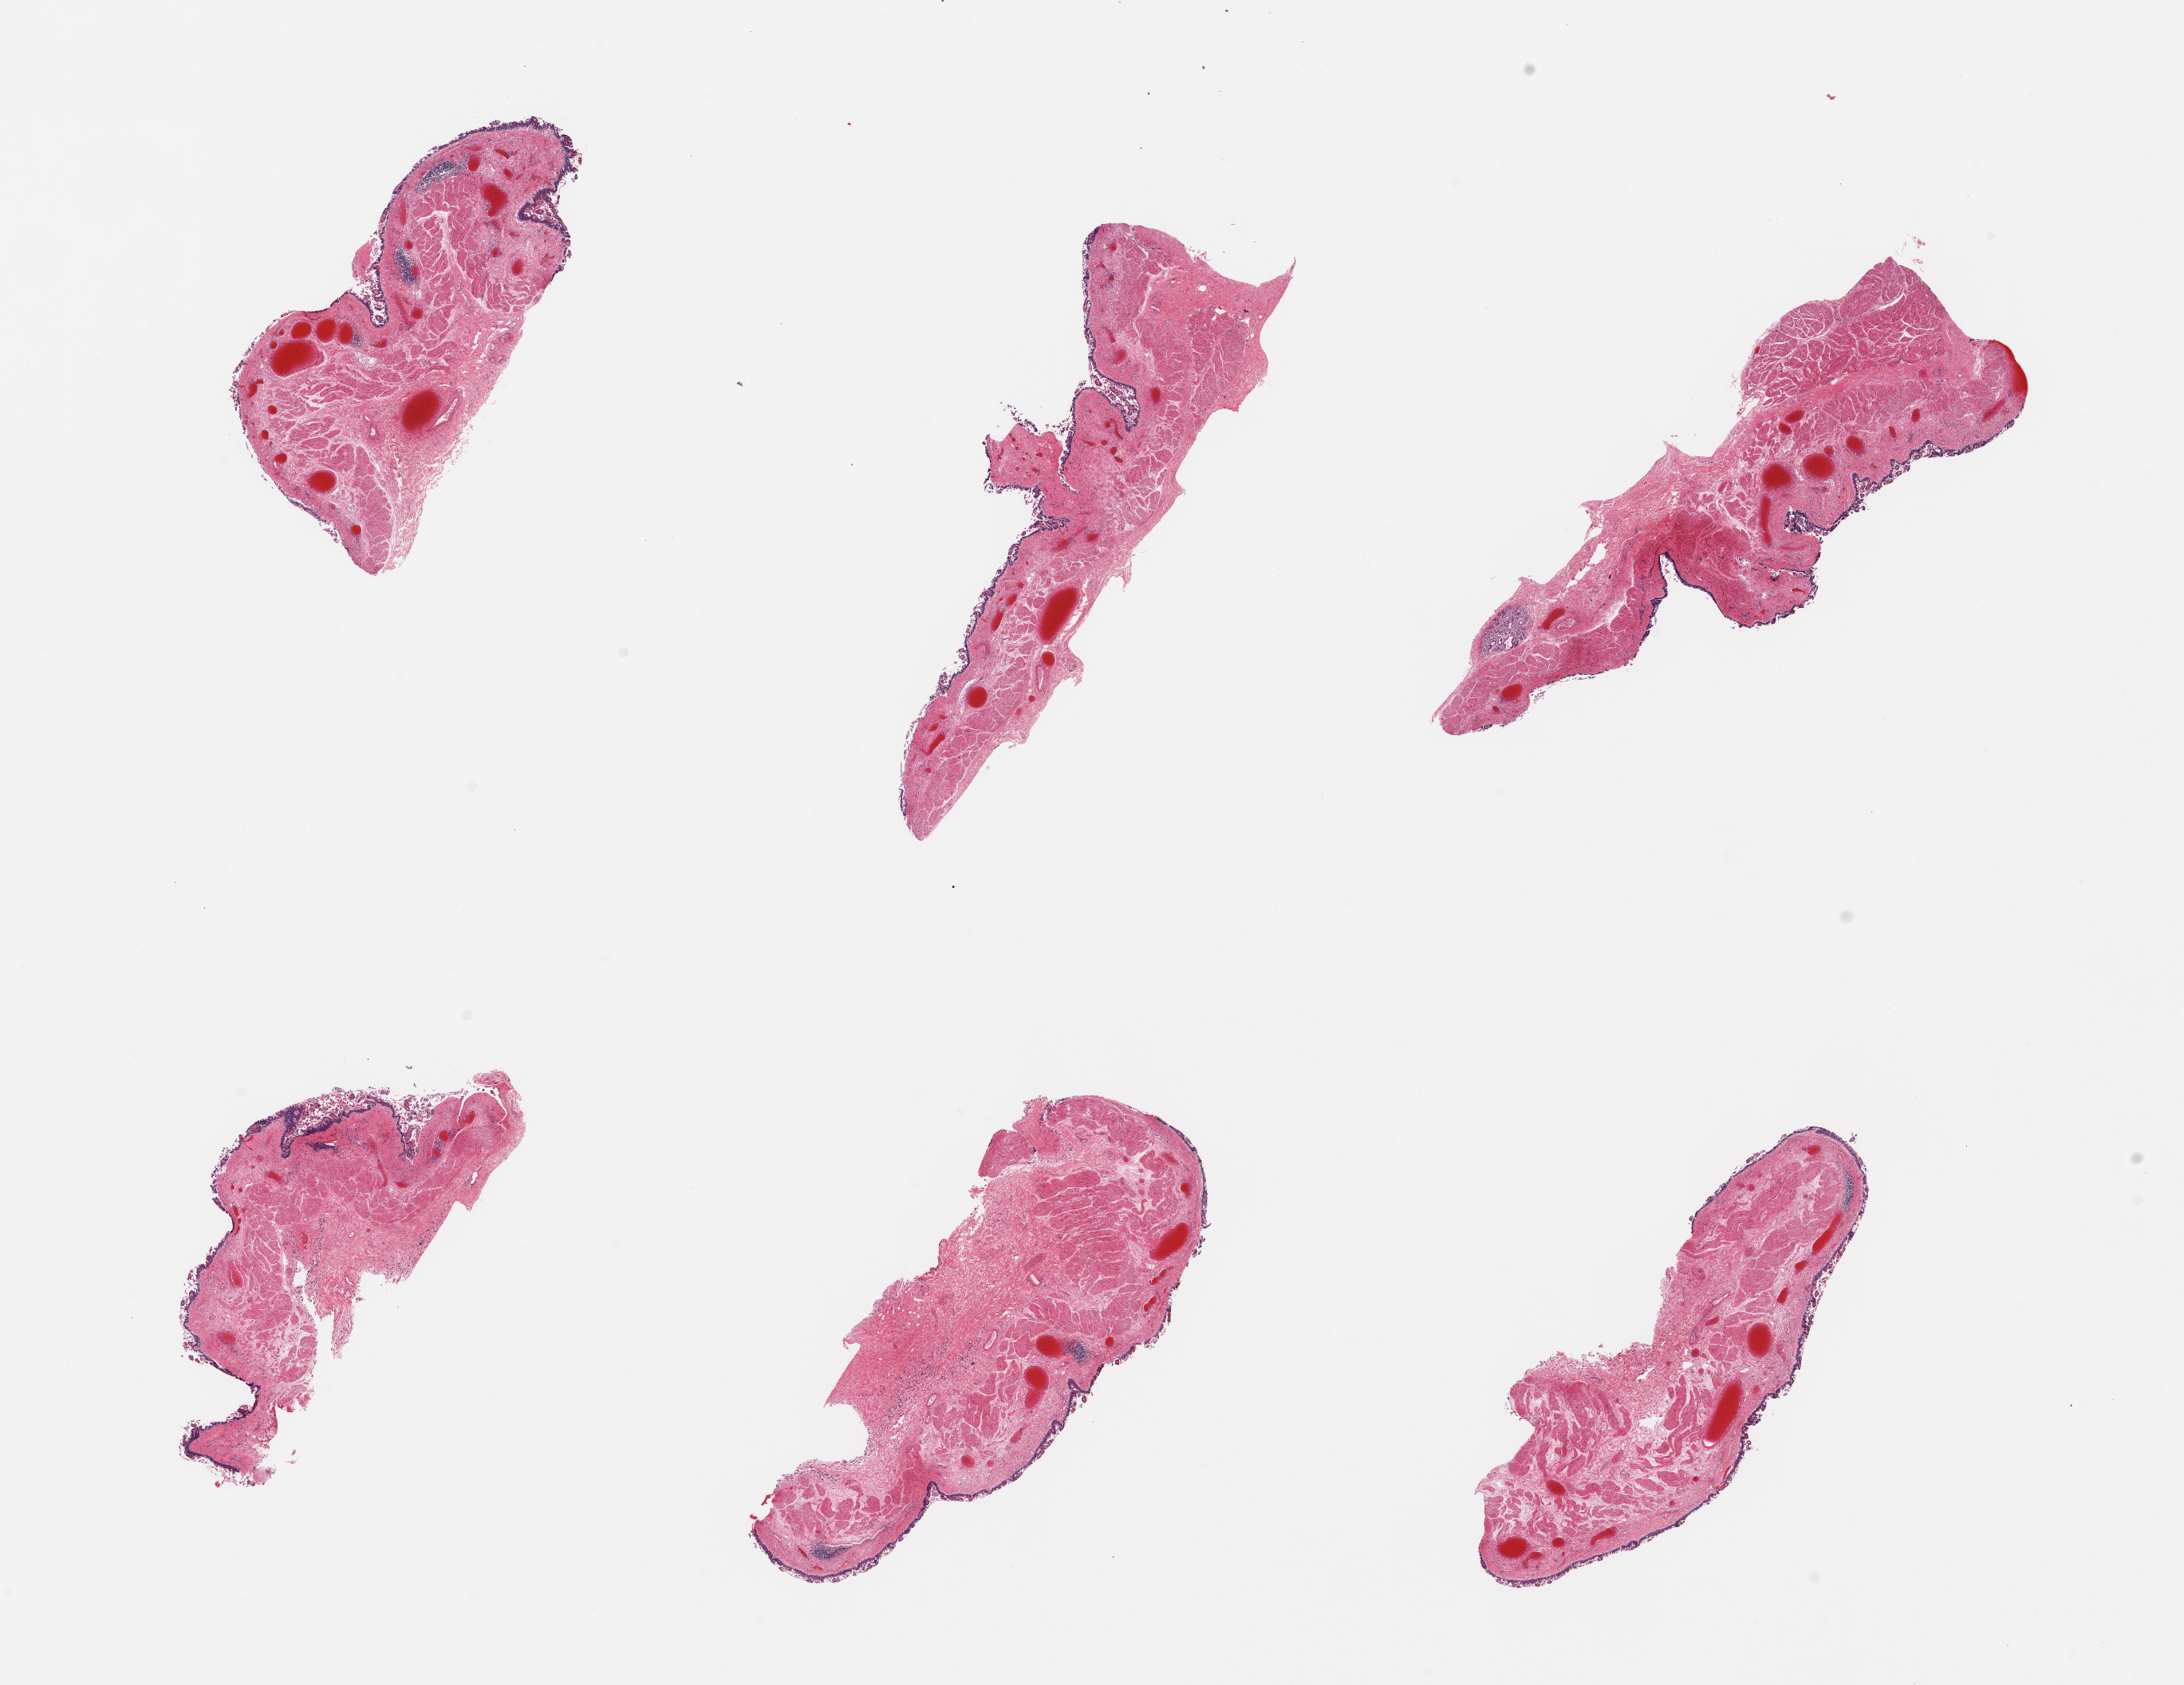
Hematoxylin and eosin (H&E) whole-slide image — whole scanned area (about 21.7 x 16.7 mm) shown as a low-resolution overview. PAXgene-fixed paraffin-embedded (PFPE) section. Sampled site (target tissue): esophageal mucous membrane. Donor tissue sample. Donor sex: female.
• pathologist's review note for this sample: 6 pieces; epithelium largely sloughed